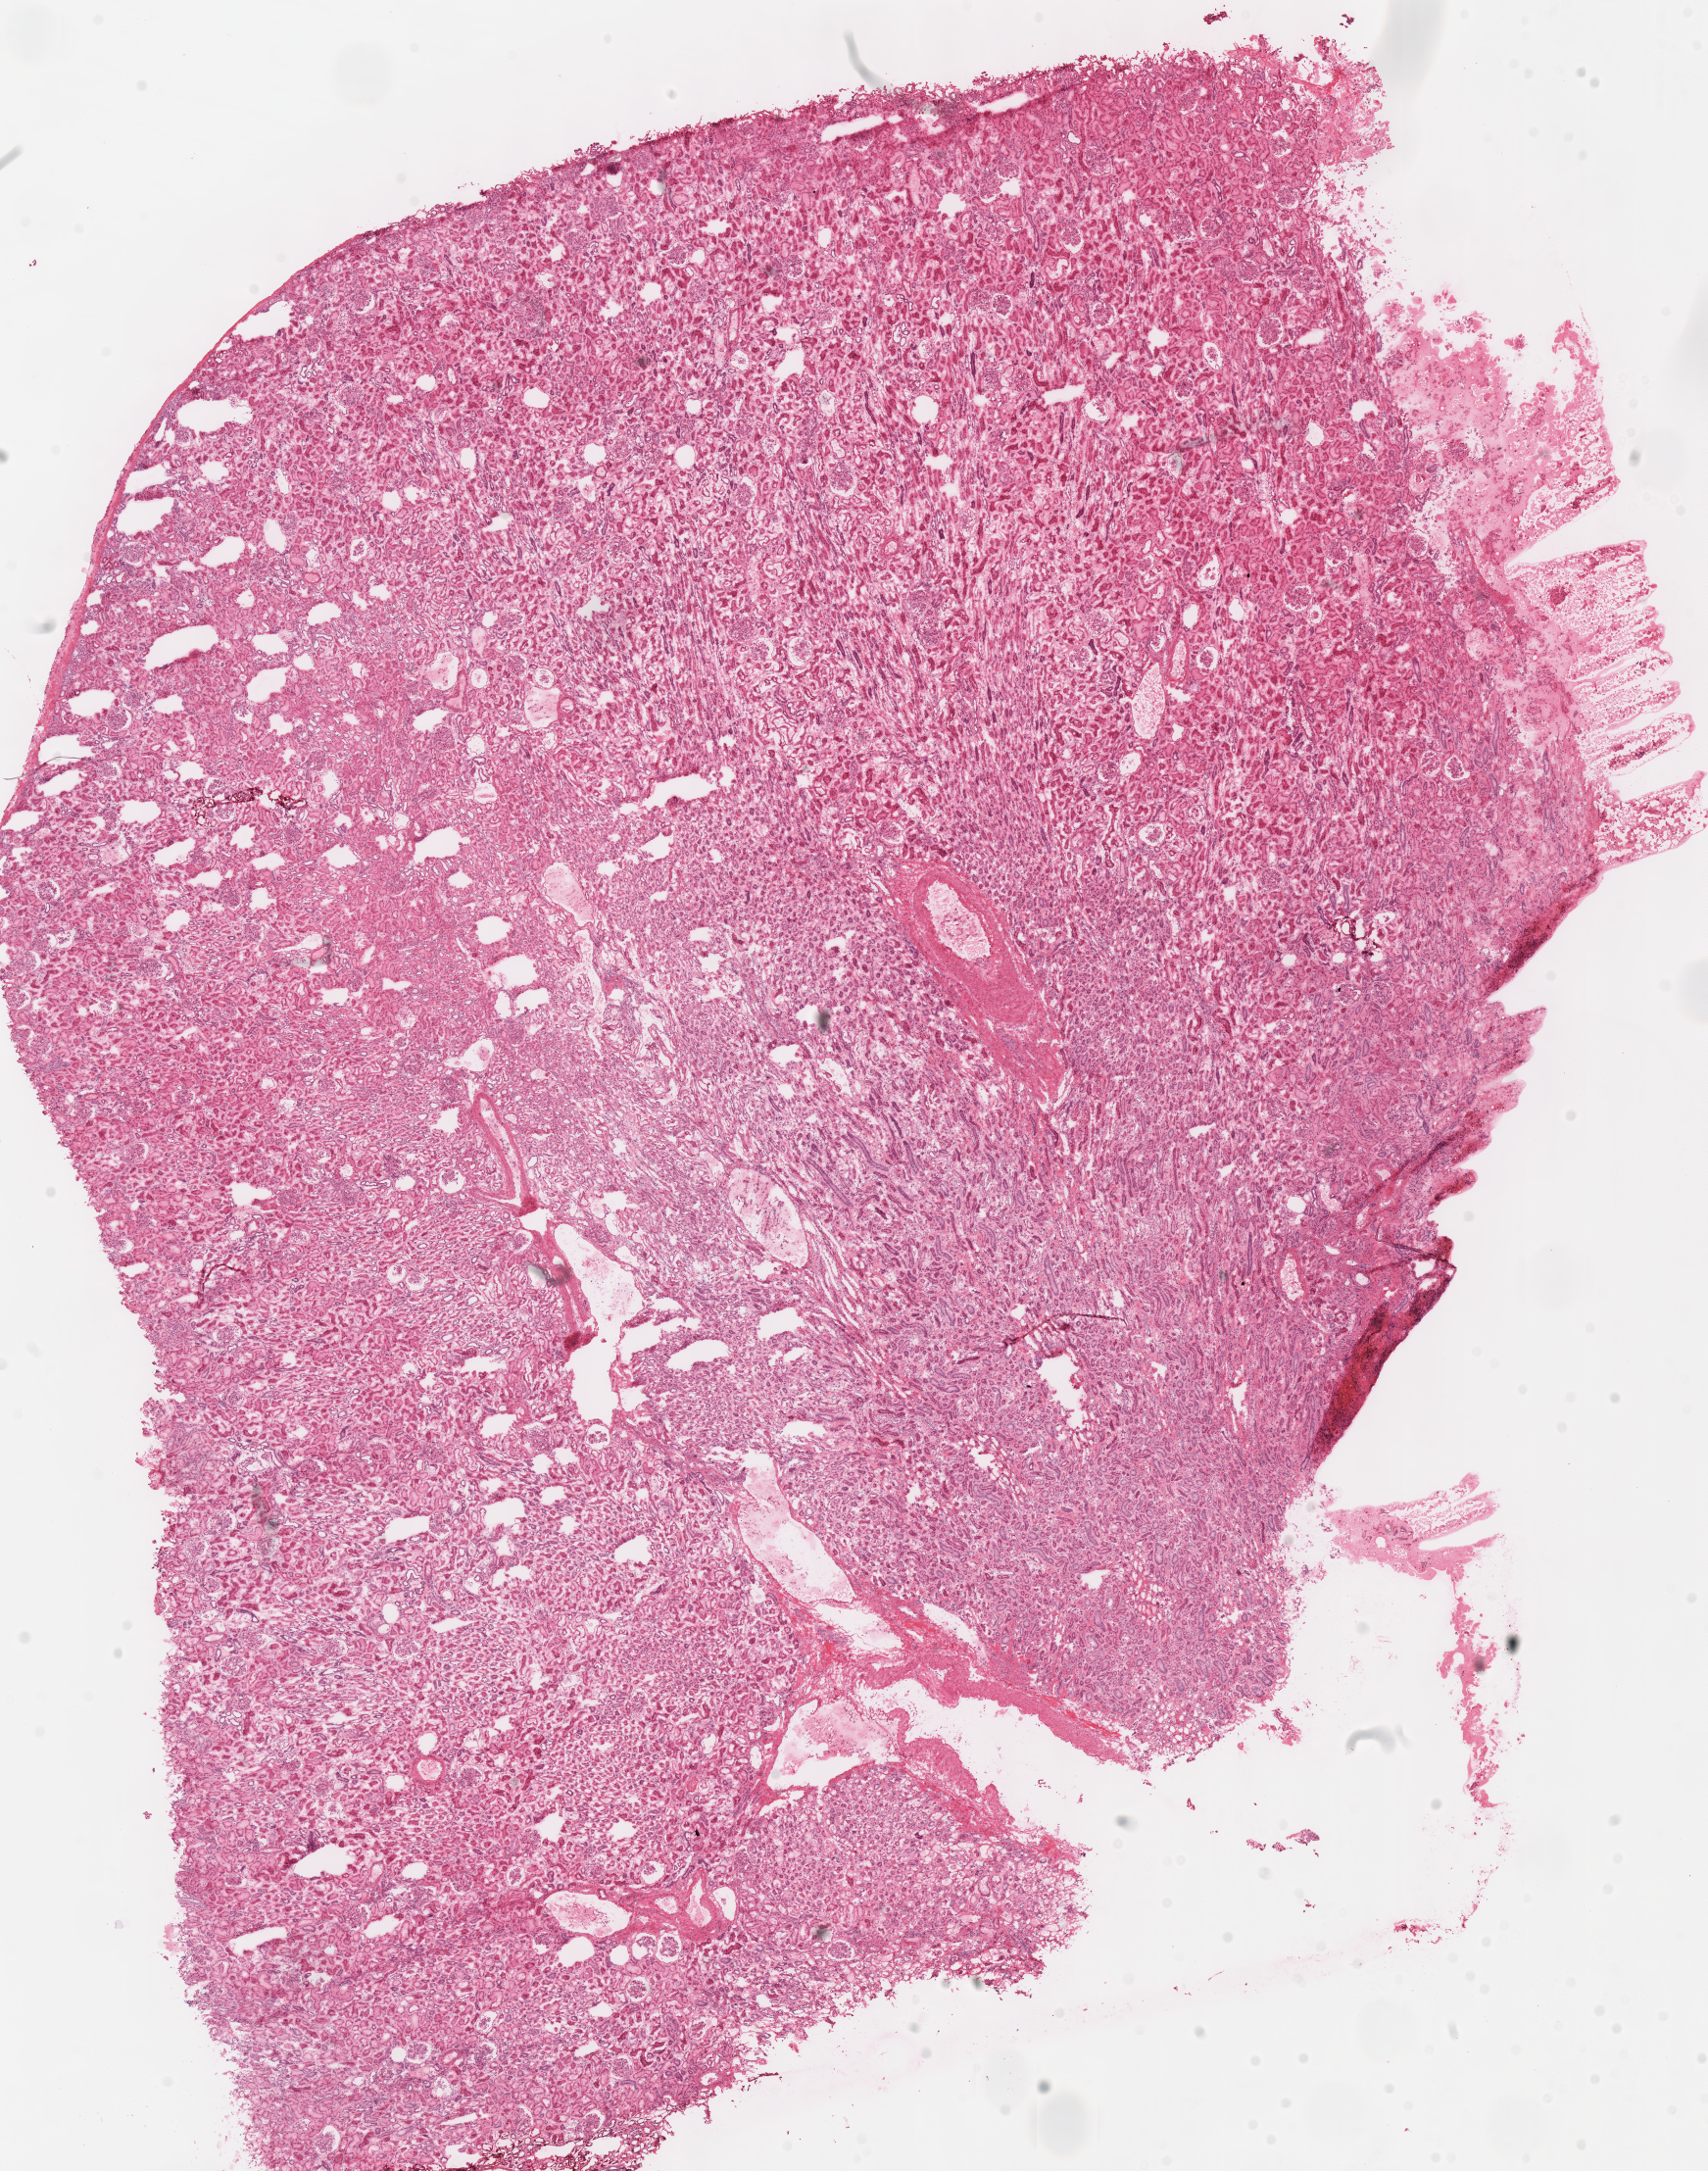
Whole-slide histology image, H&E-stained, shown as a low-resolution overview of the whole scanned area (about 13.7 x 17.4 mm, acquisition: 40x scan), frozen section from the top of the tissue portion, kidney, solid tissue normal (non-tumour tissue) sample. Female patient; age at initial diagnosis 37 years.
This section: solid tissue normal (non-tumour) sample from the same patient. Patient diagnosis: Renal cell carcinoma, chromophobe type.